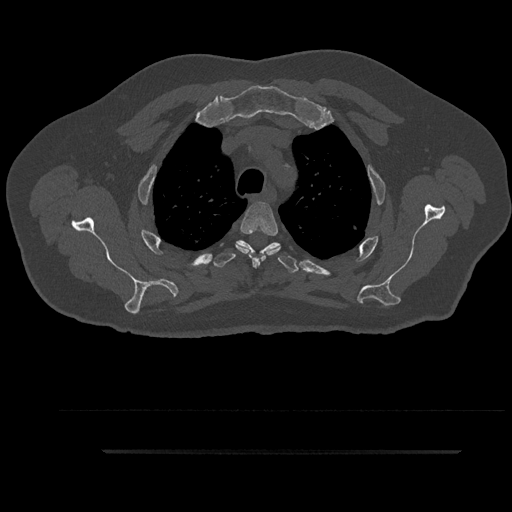
CT including the spine, one axial slice; slice 702 of 797 in the series (ordered by position); reconstruction kernel Br40s/3; 120 kVp; bone window (W 1800 / L 400 HU); 0.5 mm slice thickness; 512 × 512 image matrix, field of view 432 × 432 mm. Patient: male, 63 years. Case-level facts recorded for this patient, not image findings: primary cancer: renal; vertebrae with lytic lesions (as recorded): T8.
Outlined on this slice (semi-automatic segmentation, software-assisted and operator-edited):
- T3 vertebra: bounding box (x1, y1, x2, y2) in pixels: (235, 201, 280, 267)
- T4 vertebra: (211, 240, 299, 274)